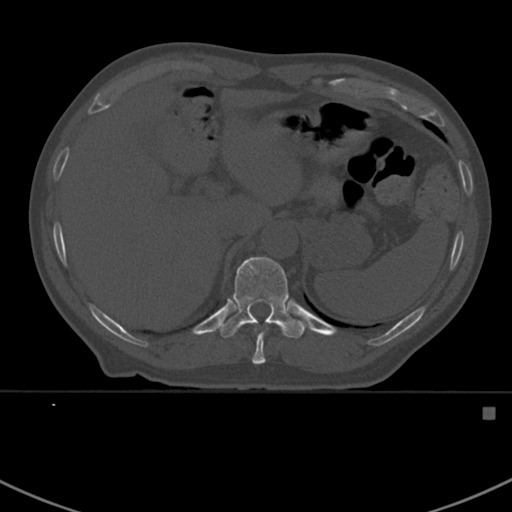
CT including the spine, one axial slice; slice 354 of 412 in the series (ordered by position); reconstruction kernel Br40s; bone window (W 1800 / L 400 HU); 1.5 mm slice thickness; 512 × 512 image matrix, field of view 358 × 358 mm. Patient: male, 59 years. From the clinical record (not read from this slice): primary cancer: prostate.
Annotated regions visible in this slice (semi-automatic segmentation, software-assisted and operator-edited):
- T10 vertebra: bounding box [x1, y1, x2, y2] px = [252, 329, 267, 364]
- T11 vertebra: [218, 257, 305, 338]